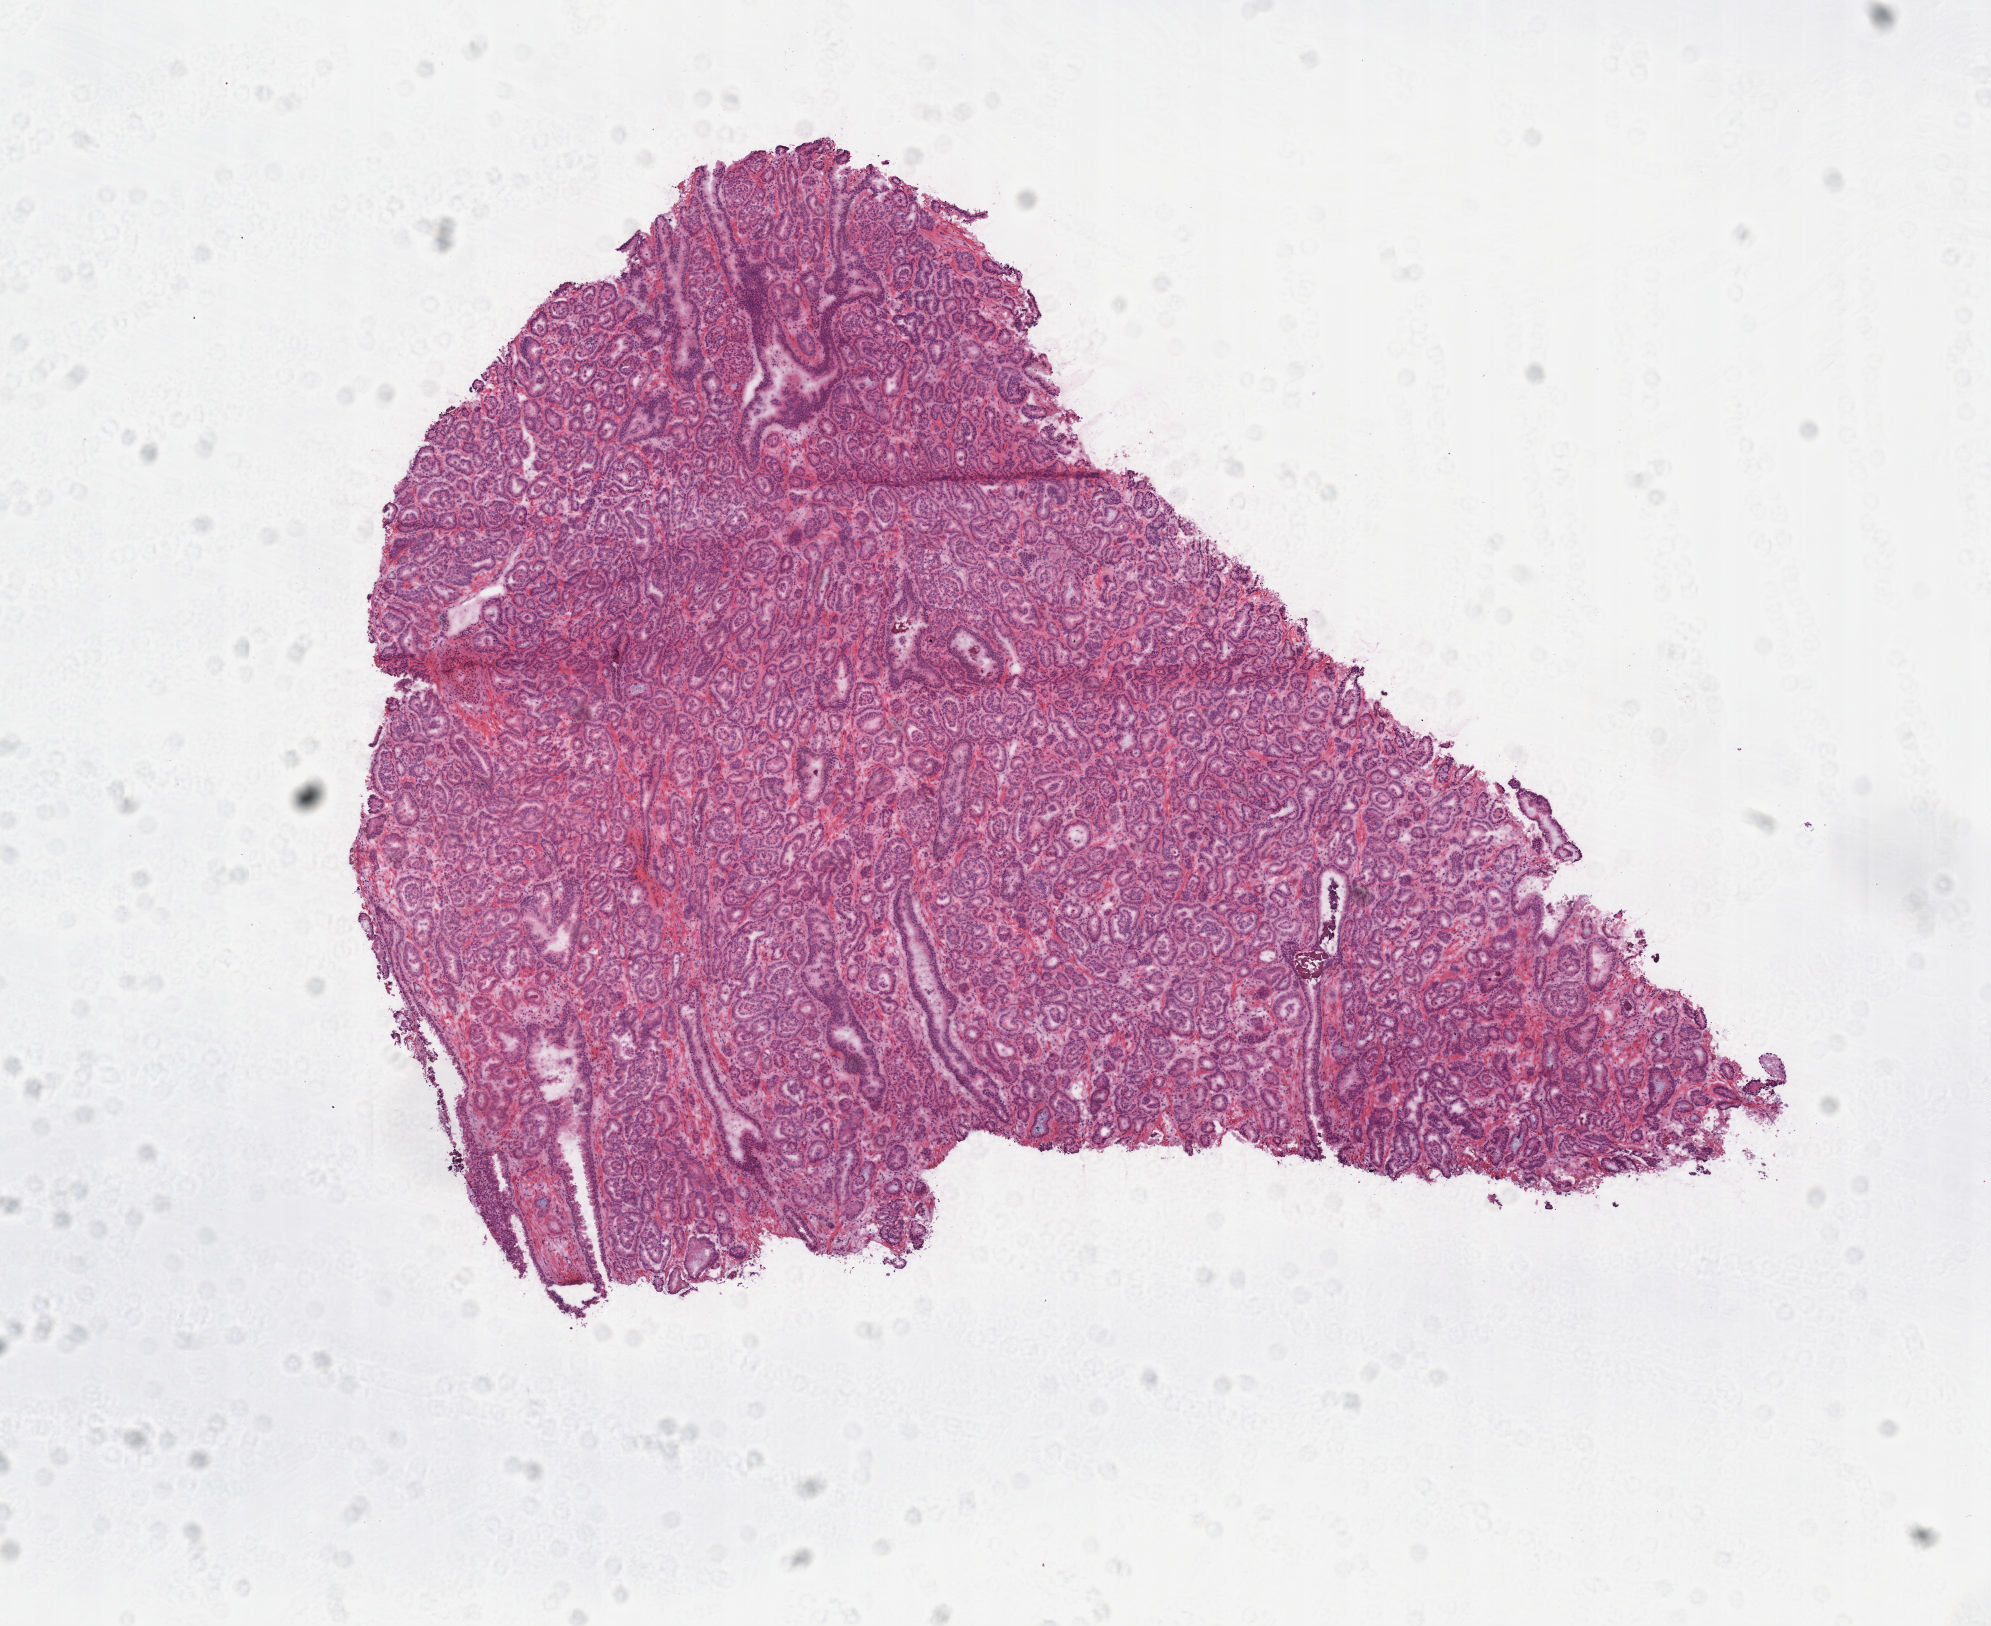
Digitized Hematoxylin and eosin (H&E) stained tissue section (whole slide) — a low-resolution overview of the entire scanned area, about 8.1 x 6.6 mm; frozen section from the top of the tissue portion; primary tumour sample from the prostate. Patient: male, age at initial diagnosis 49 years. Gleason score: 6 (3+3). Slide review estimates, as recorded: tumour cells 100%, tumour nuclei 80%, normal cells 0%, stromal cells 0%, necrosis 0%. Inflammatory infiltration, as recorded: lymphocyte infiltration 0%, monocyte infiltration 0%, neutrophil infiltration 0%.
Laterality: bilateral. Histologic diagnosis: Adenocarcinoma, NOS (prostate gland).